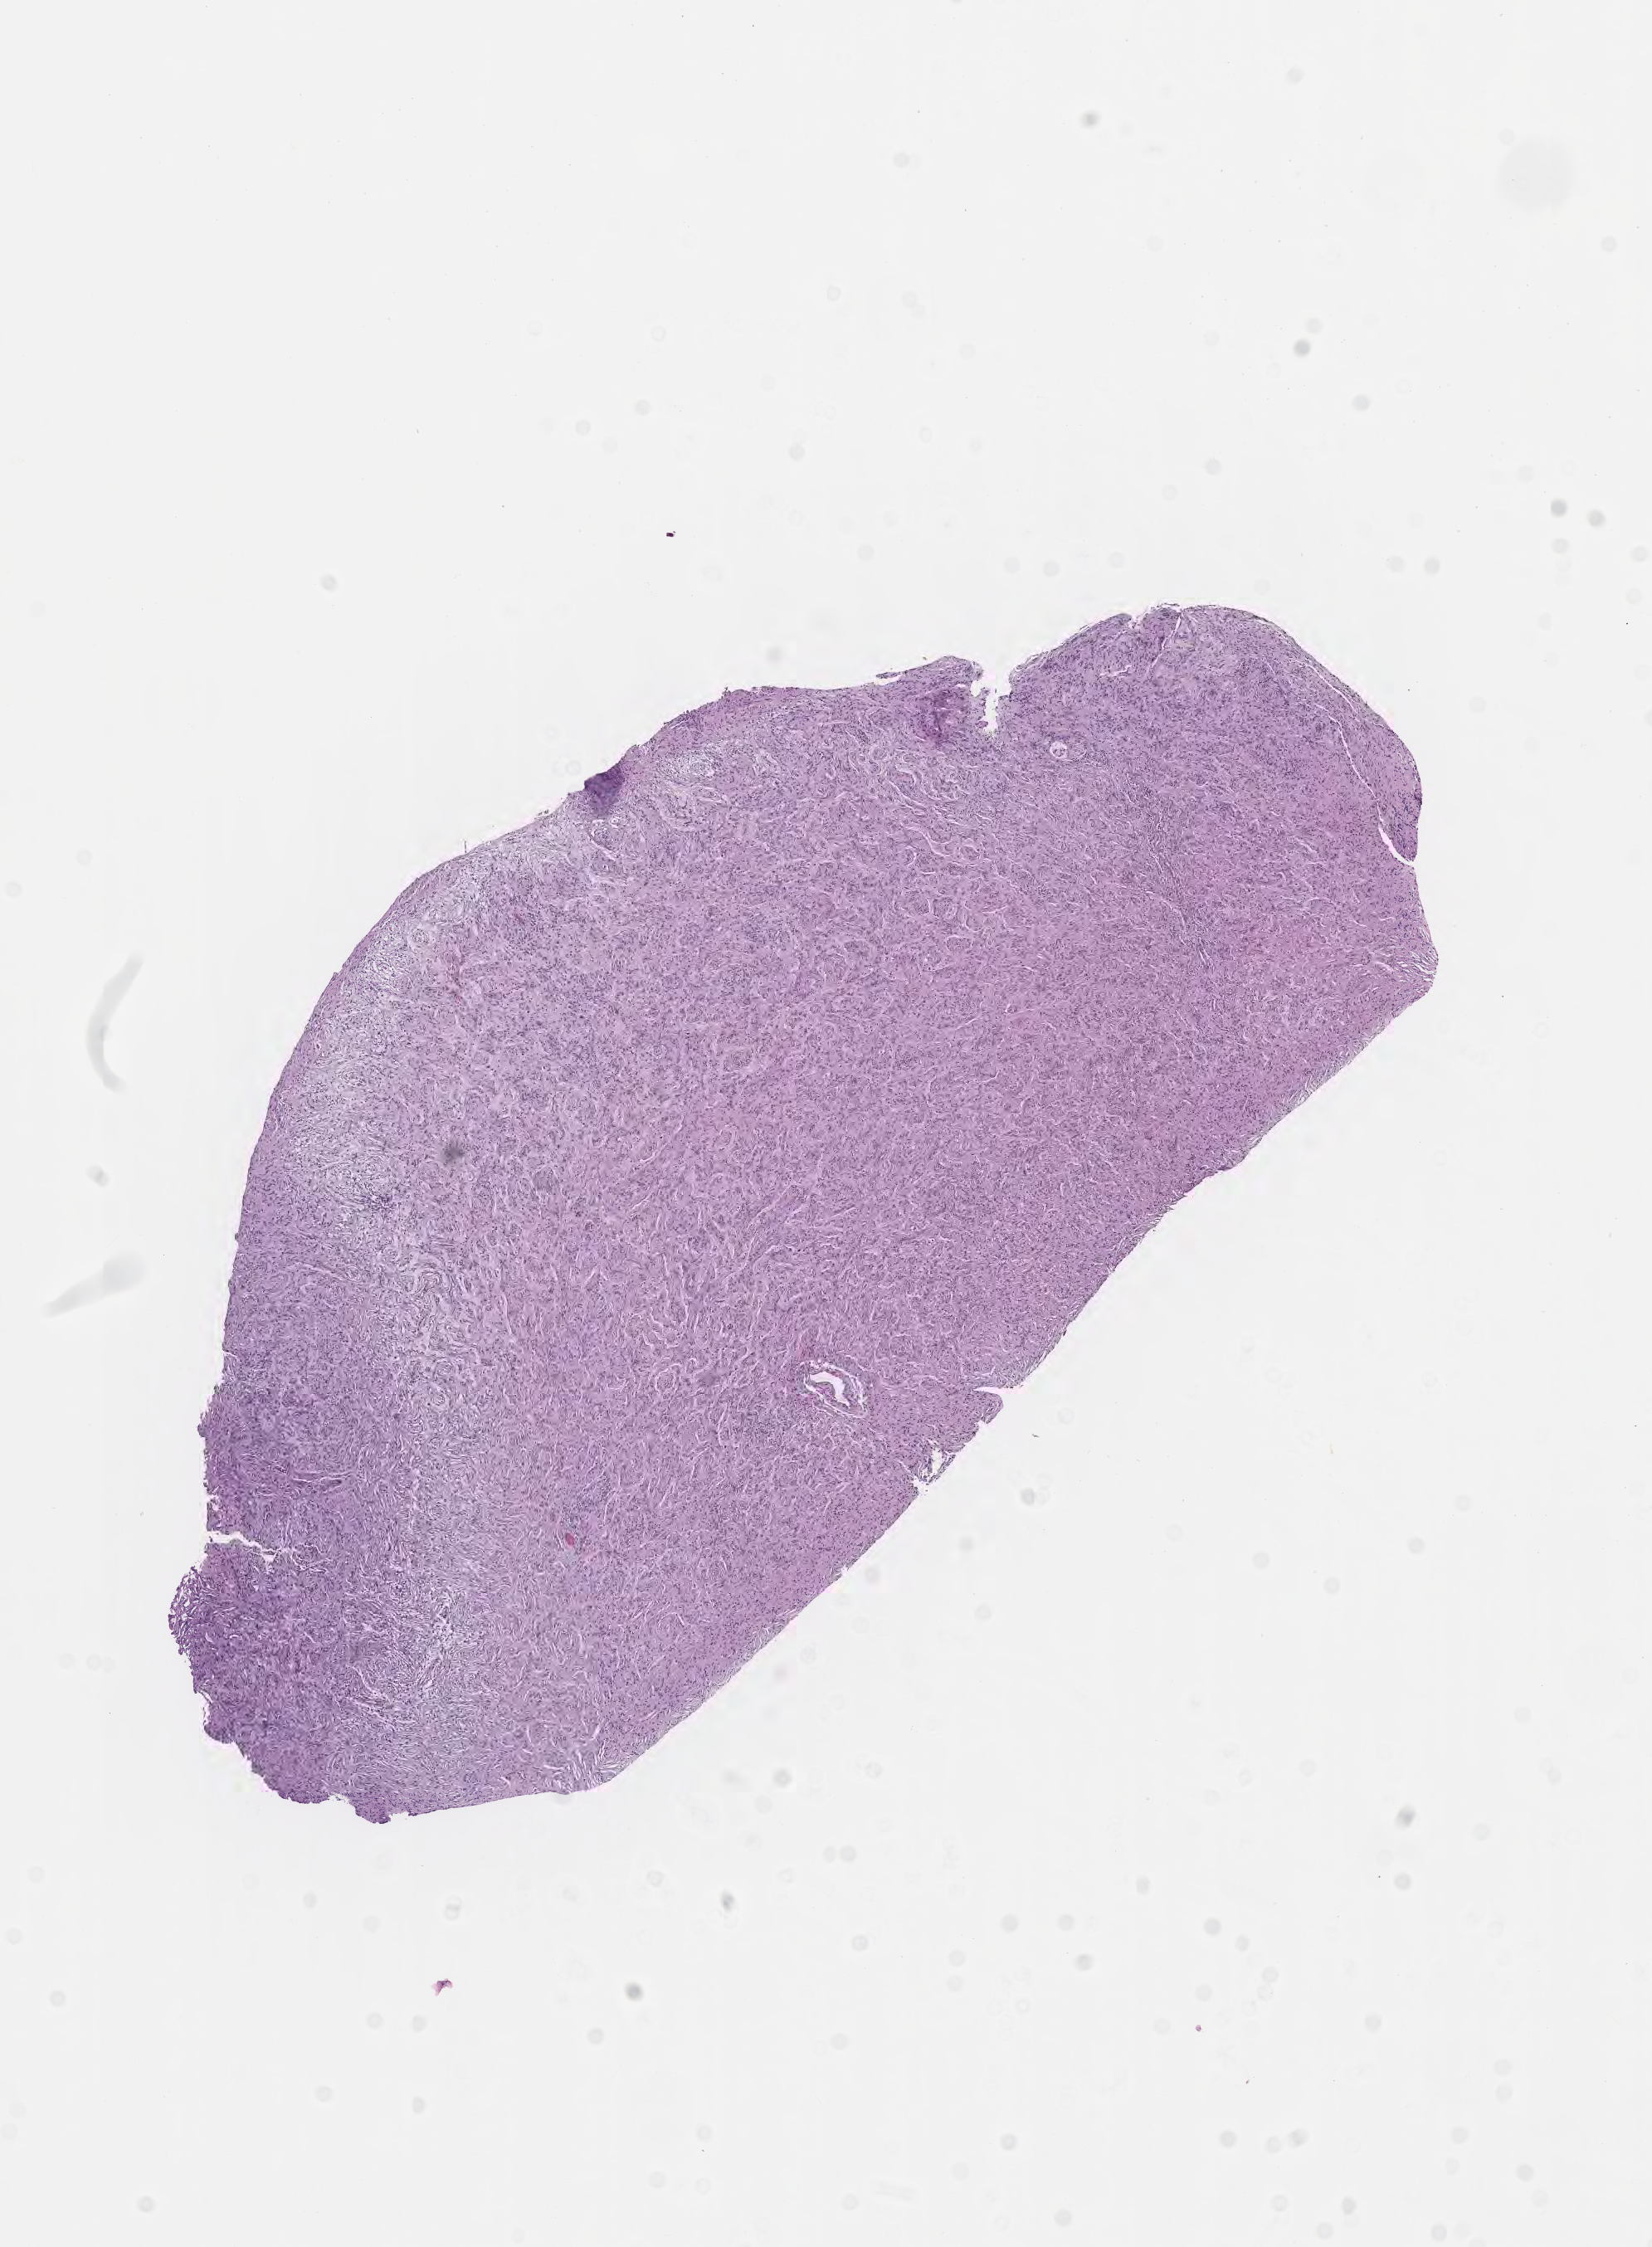
Hematoxylin and eosin (H&E) whole-slide image of tumor tissue from the temporal lobe — a low-resolution overview of the entire scanned area, about 8.1 x 10.9 mm. Formalin-fixed, paraffin-embedded (FFPE) tissue. Patient male; age 138 months (11 years 6 months).
Diagnosis: Meningiomatosis, NOS.